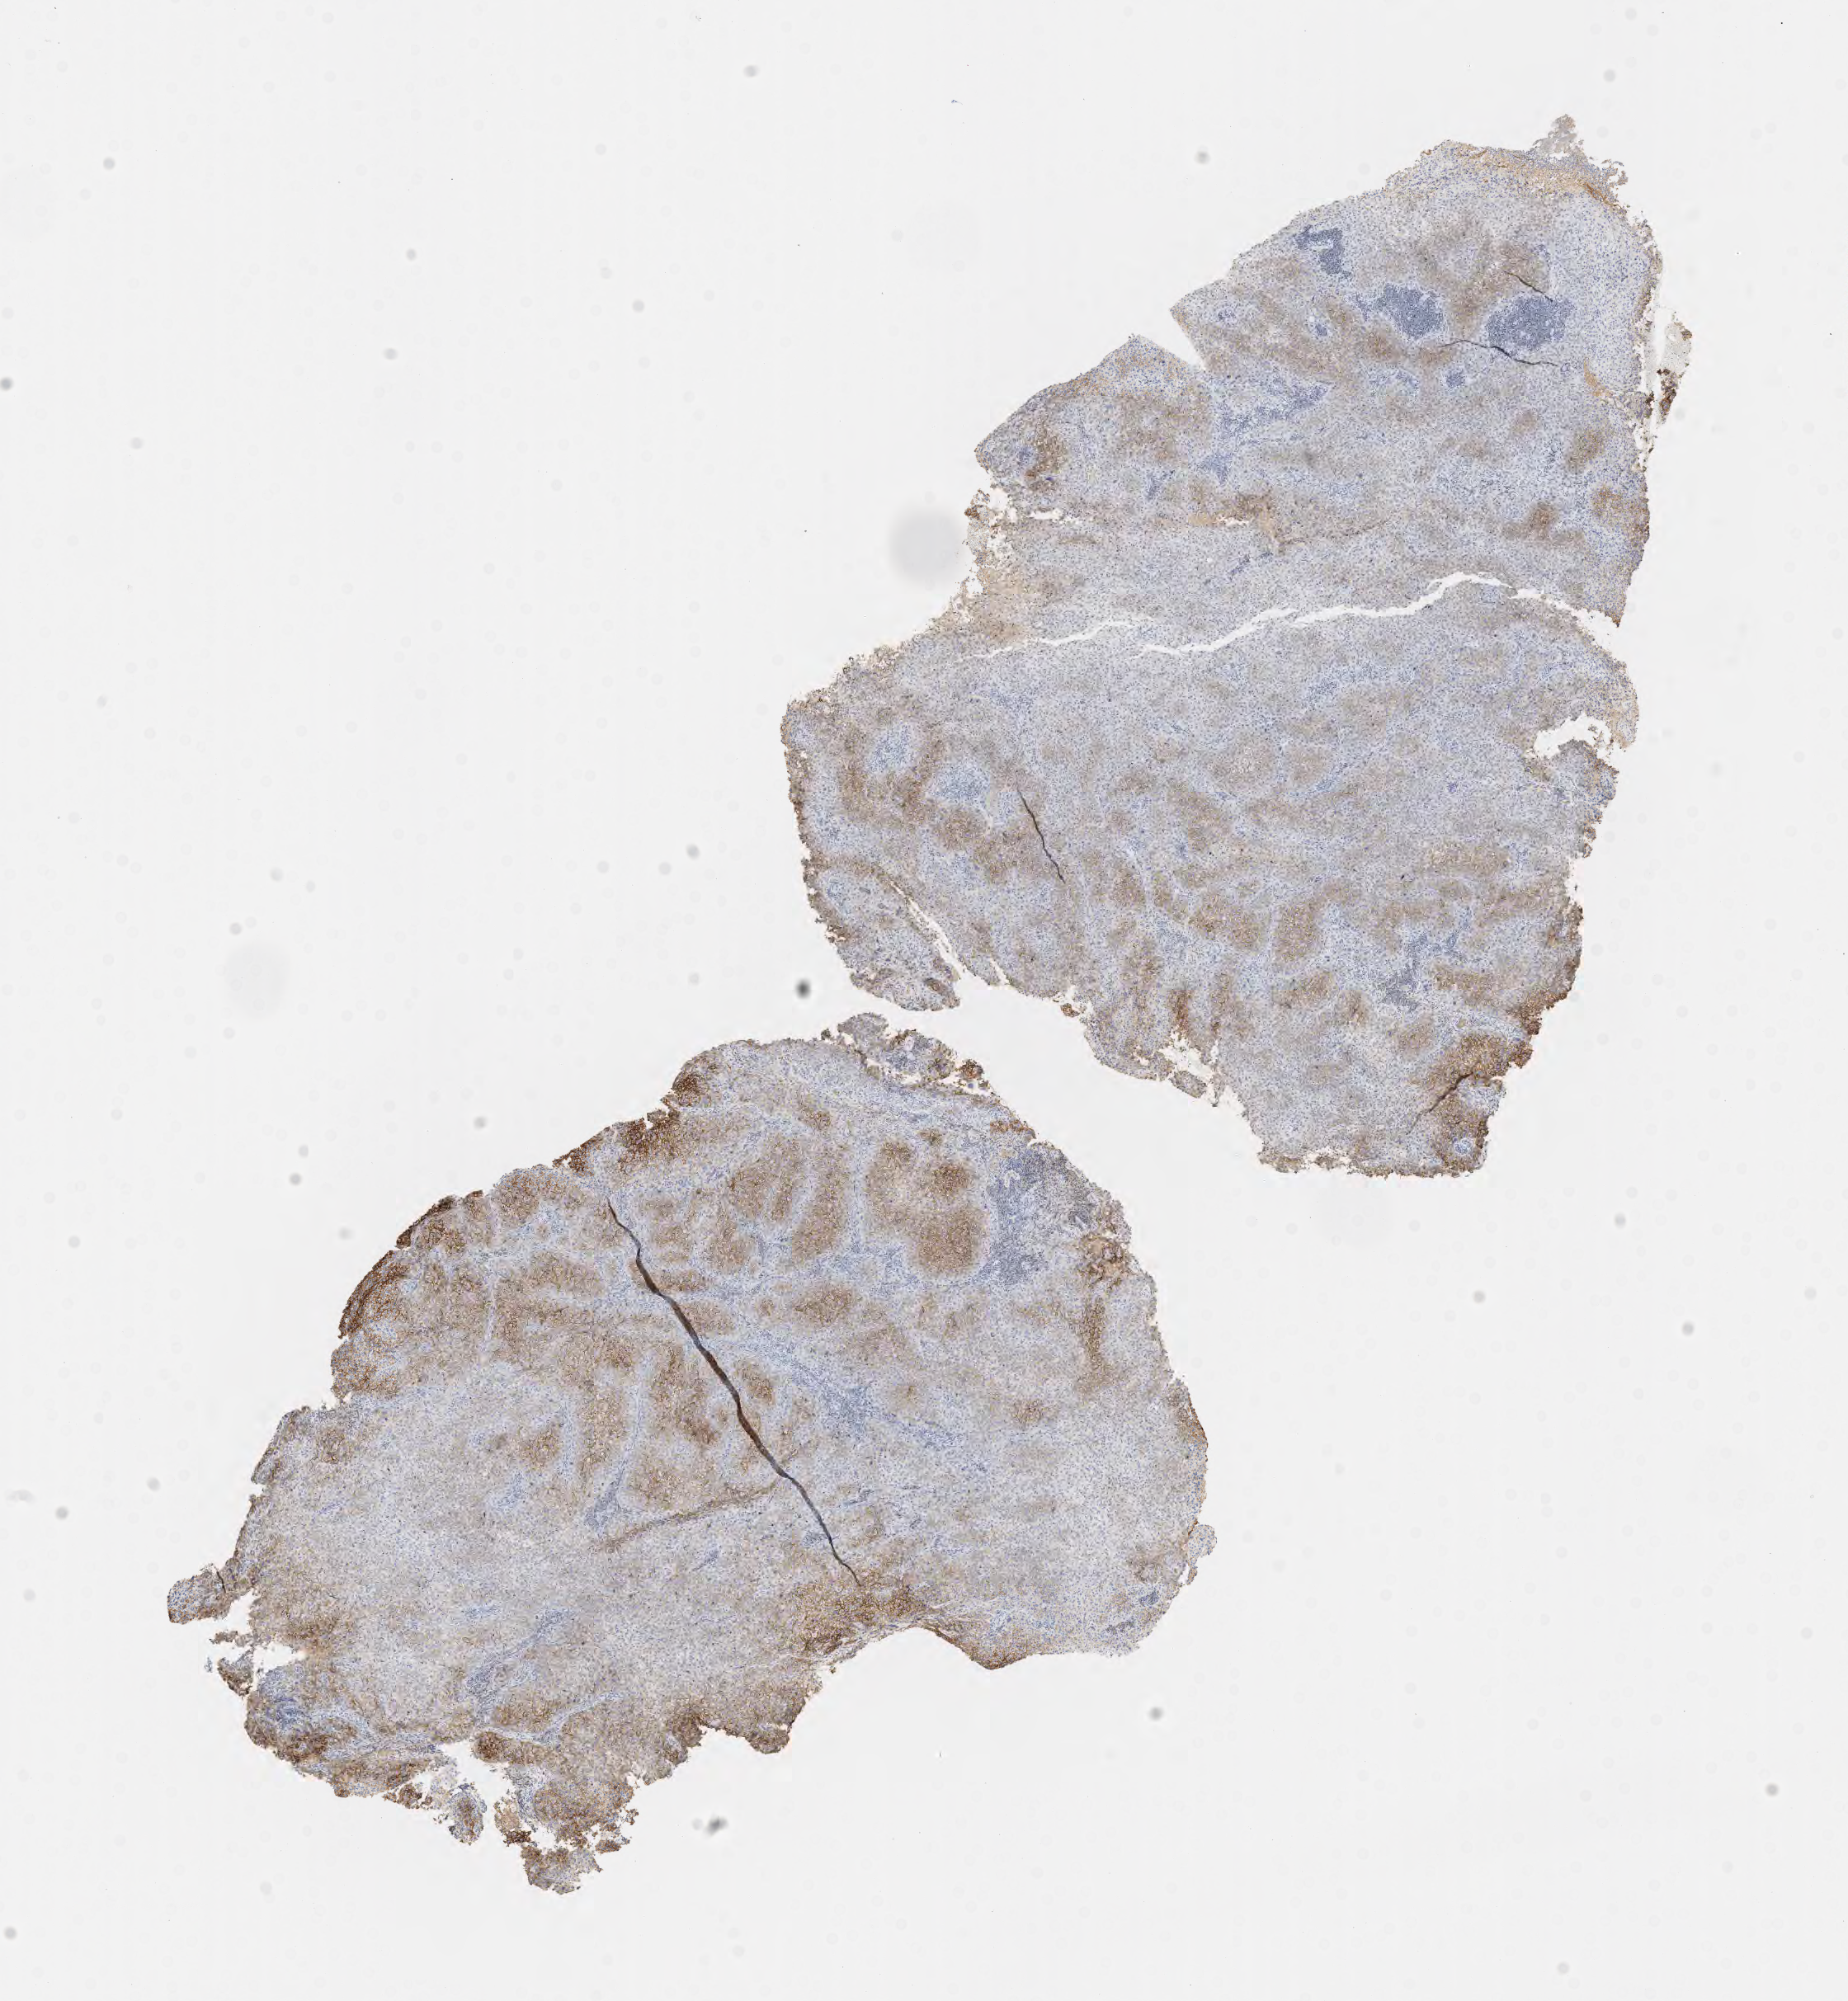
Whole-slide image, immunohistochemical stain for Ber-EP4 — low-resolution overview of the scanned area, about 9.1 x 9.8 mm, tumor tissue, anatomic site: cervix. Patient: female, age 45 years.
Diagnosis: Squamous cell carcinoma, large cell, nonkeratinizing, NOS.